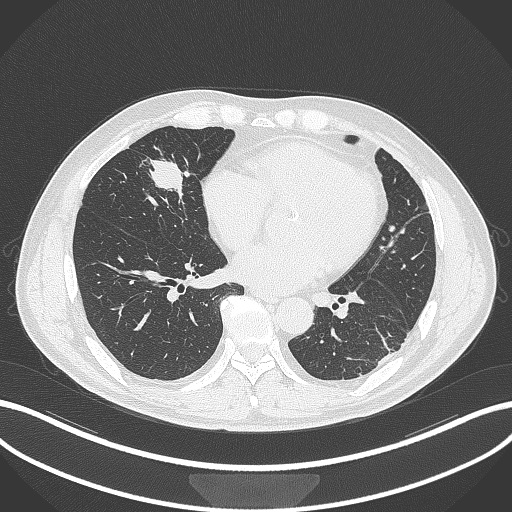
Chest CT, one axial slice. Position 110 of 399 along the scan axis. Reconstruction kernel B70f. Lung window (W 1500 / L -600 HU). 1 mm slice thickness. 512 × 512 image matrix. Male patient, age 59 years. Case-level facts recorded for this patient, not image findings: clinical TNM (as recorded): T2a N1 M0.
Annotated regions visible in this slice (rectangle marked by the reading radiologist):
- lung tumour (recorded histology: adenocarcinoma): bounding box [x1, y1, x2, y2] px = [141, 150, 188, 196]